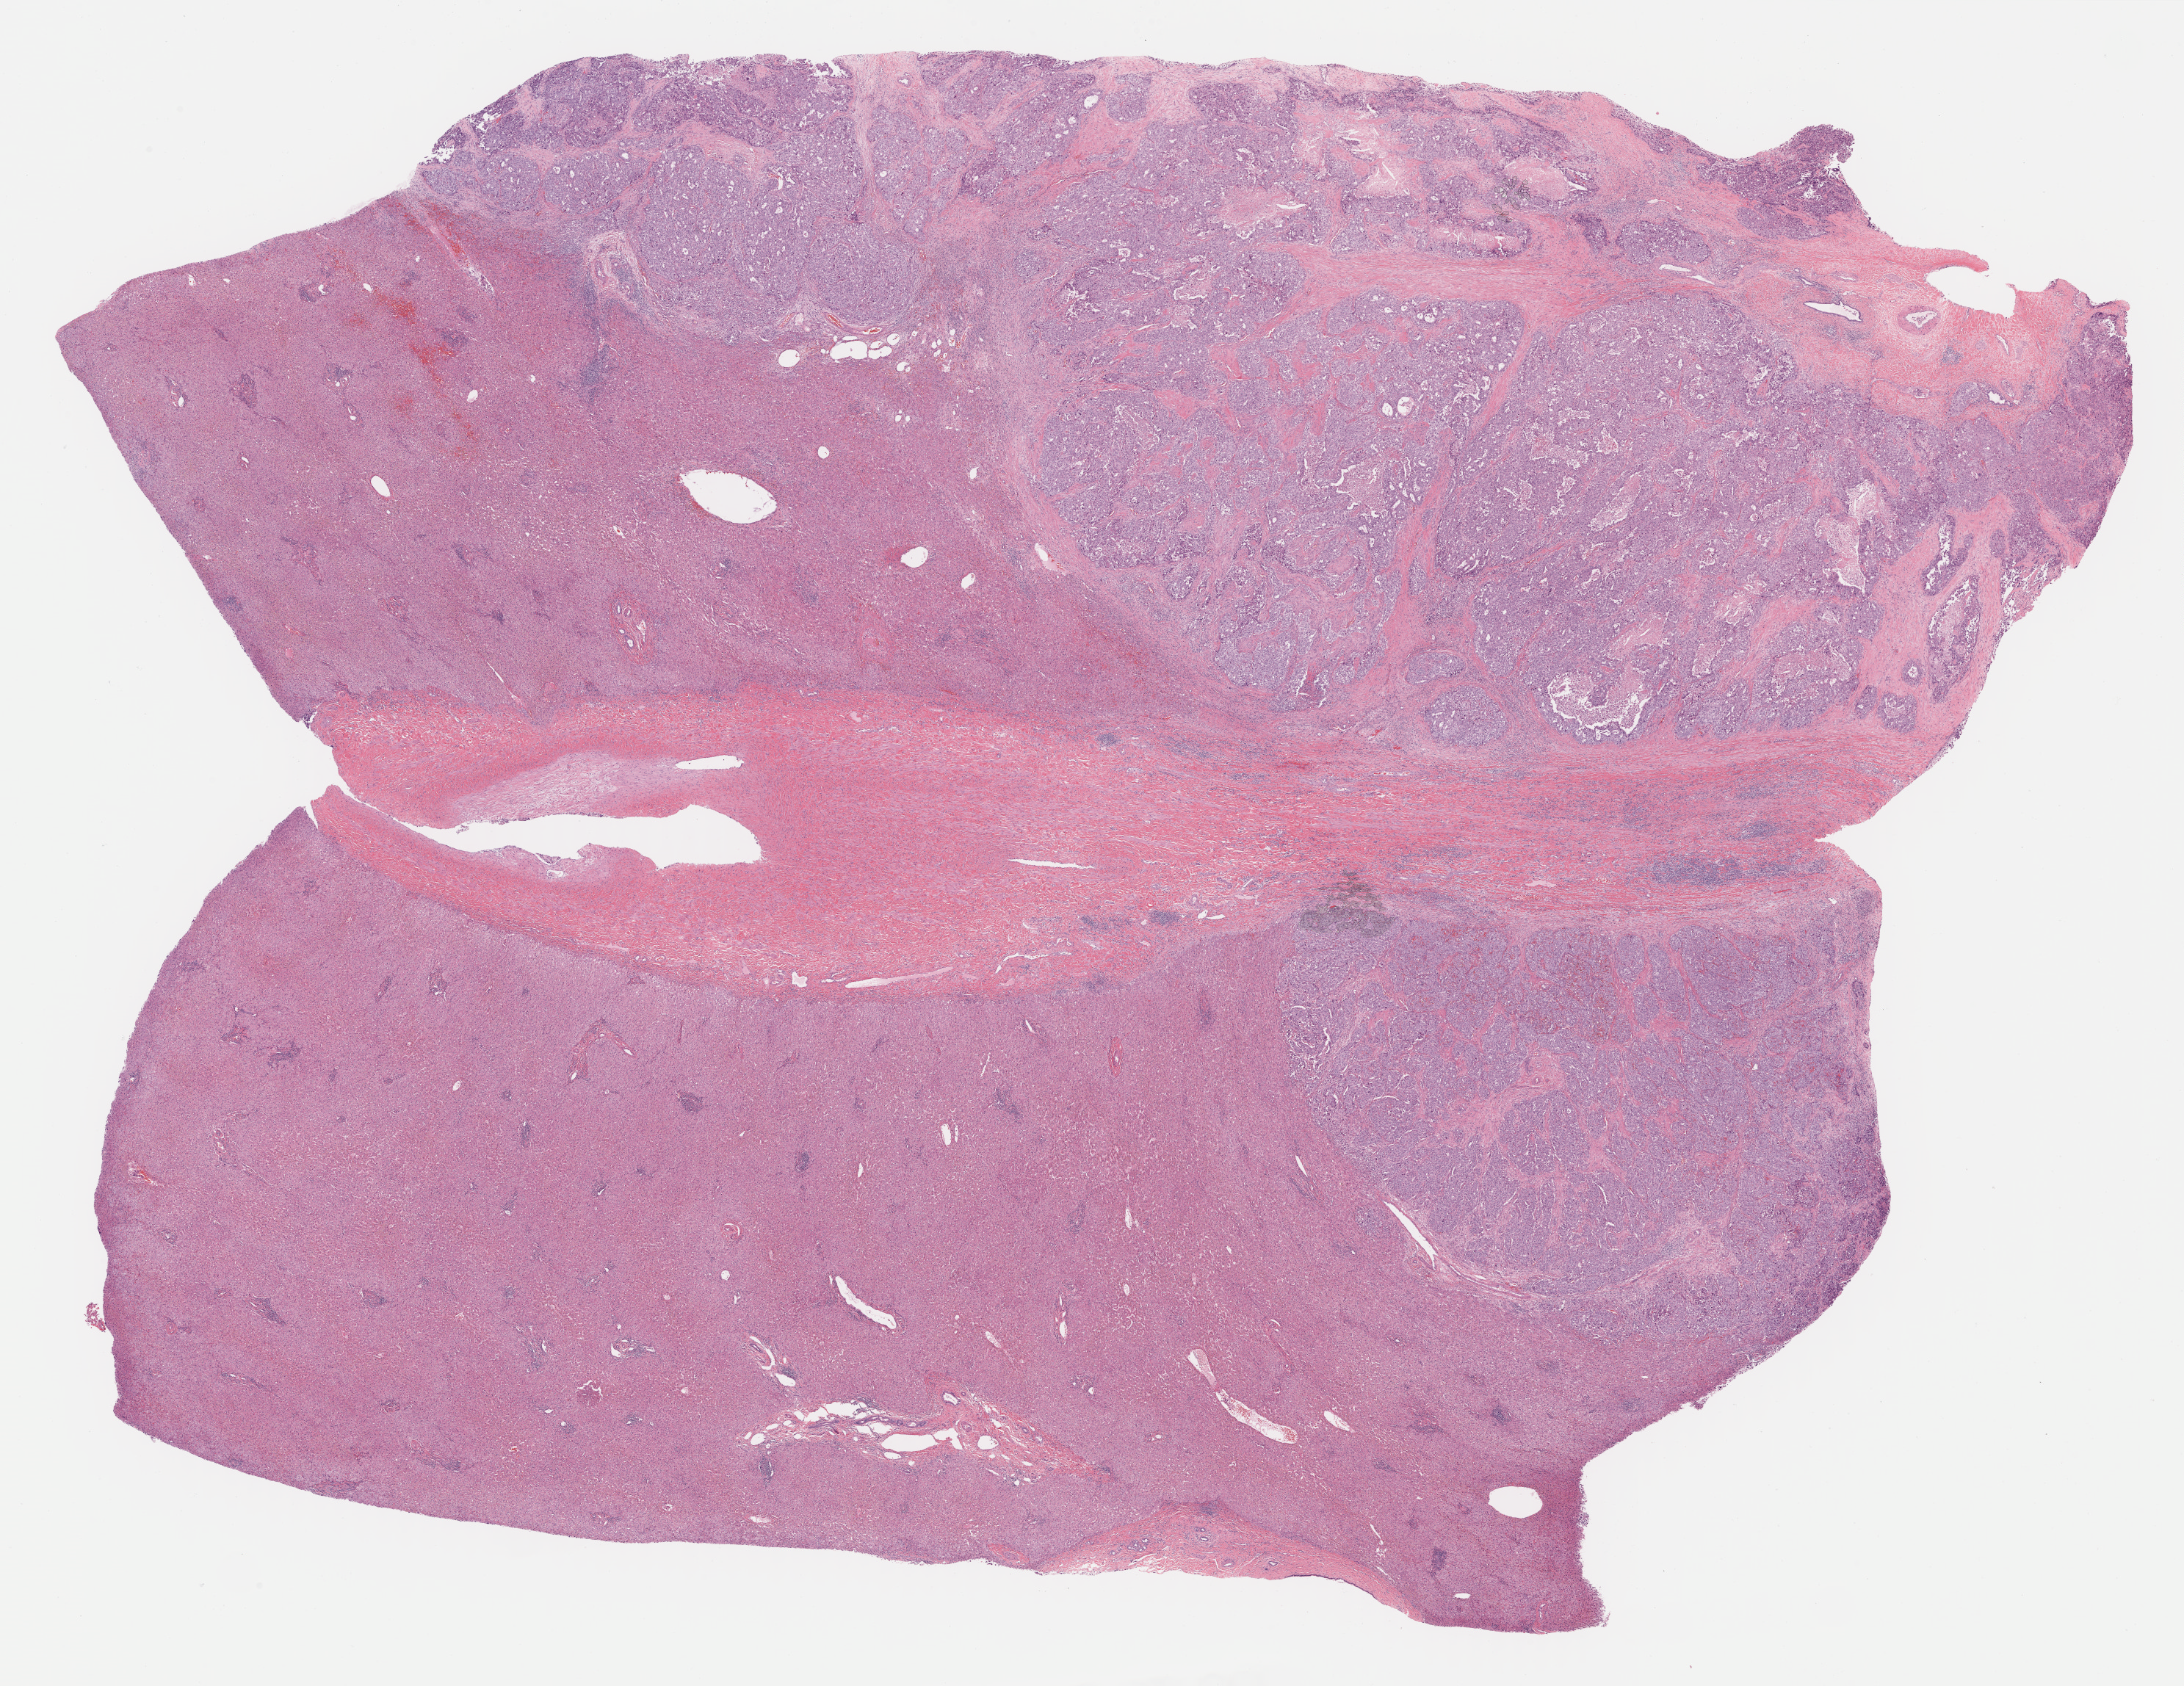
Whole-slide histology image, H&E-stained — a low-resolution overview of the entire scanned area, about 24.1 x 18.6 mm; formalin-fixed paraffin-embedded (FFPE) diagnostic section; bile duct, primary tumour sample. Female, age 55 years at initial diagnosis. Histologic grade: G3 (poorly differentiated).
Histologic diagnosis: Cholangiocarcinoma (intrahepatic bile duct). AJCC pathologic stage: I (7th edition).